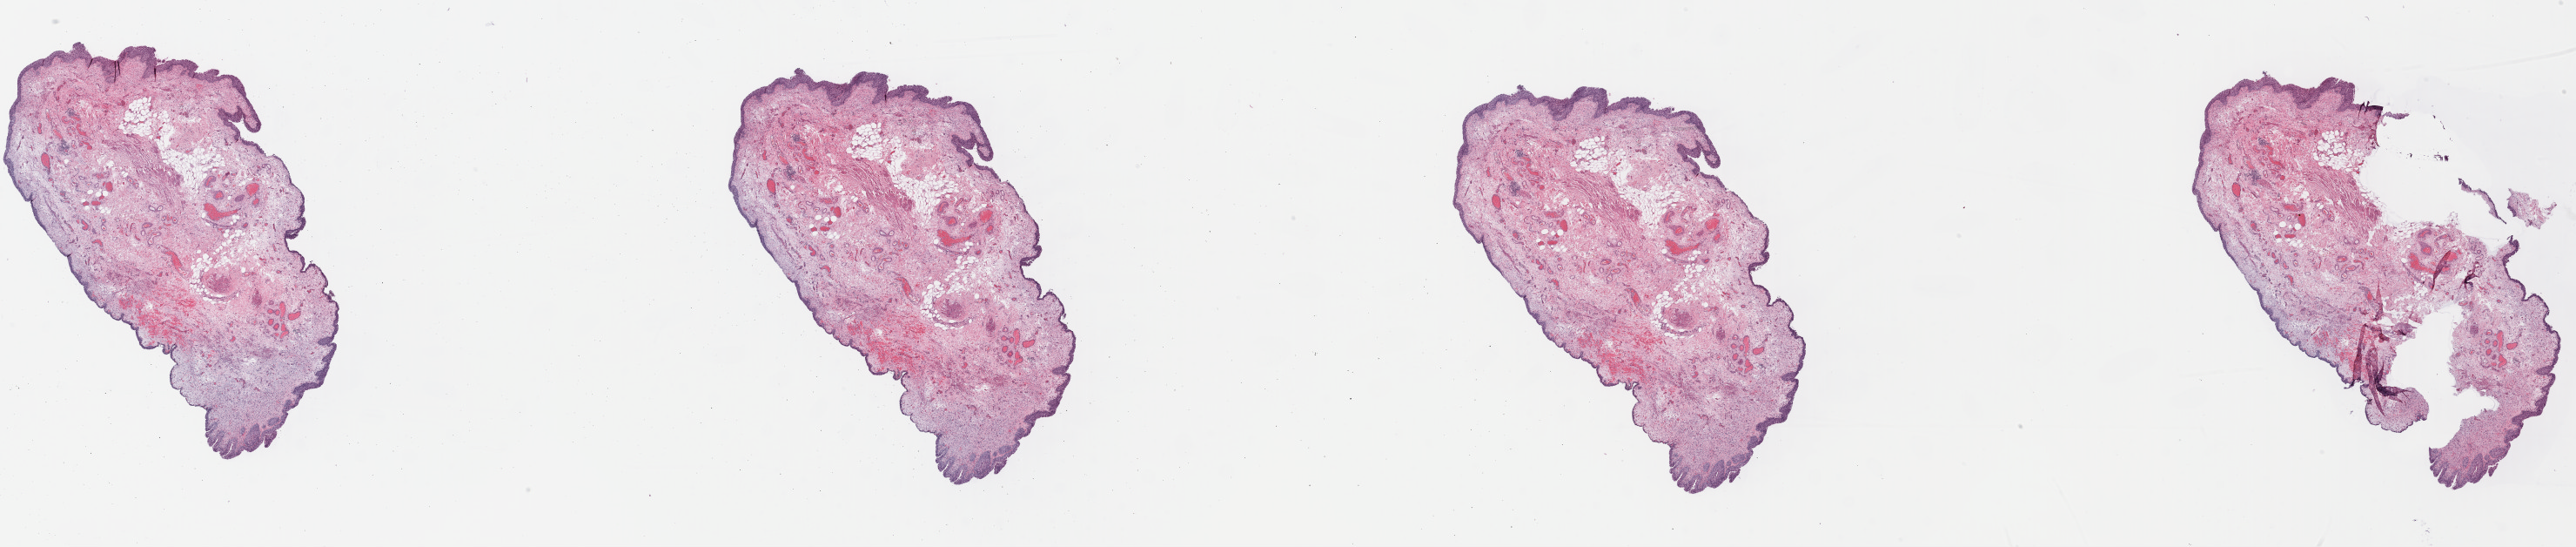
Whole-slide histology image, H&E — shown as a low-resolution overview of the whole scanned area (about 46.5 x 9.9 mm); formalin-fixed paraffin-embedded (FFPE) diagnostic section; sample: primary tumour, bladder. Female patient; age at initial diagnosis 80 years. Histologic grade: high grade.
Pathologic diagnosis: Transitional cell carcinoma (posterior wall of bladder). AJCC pathologic stage: III (7th edition). TNM: T4a N0 MX.